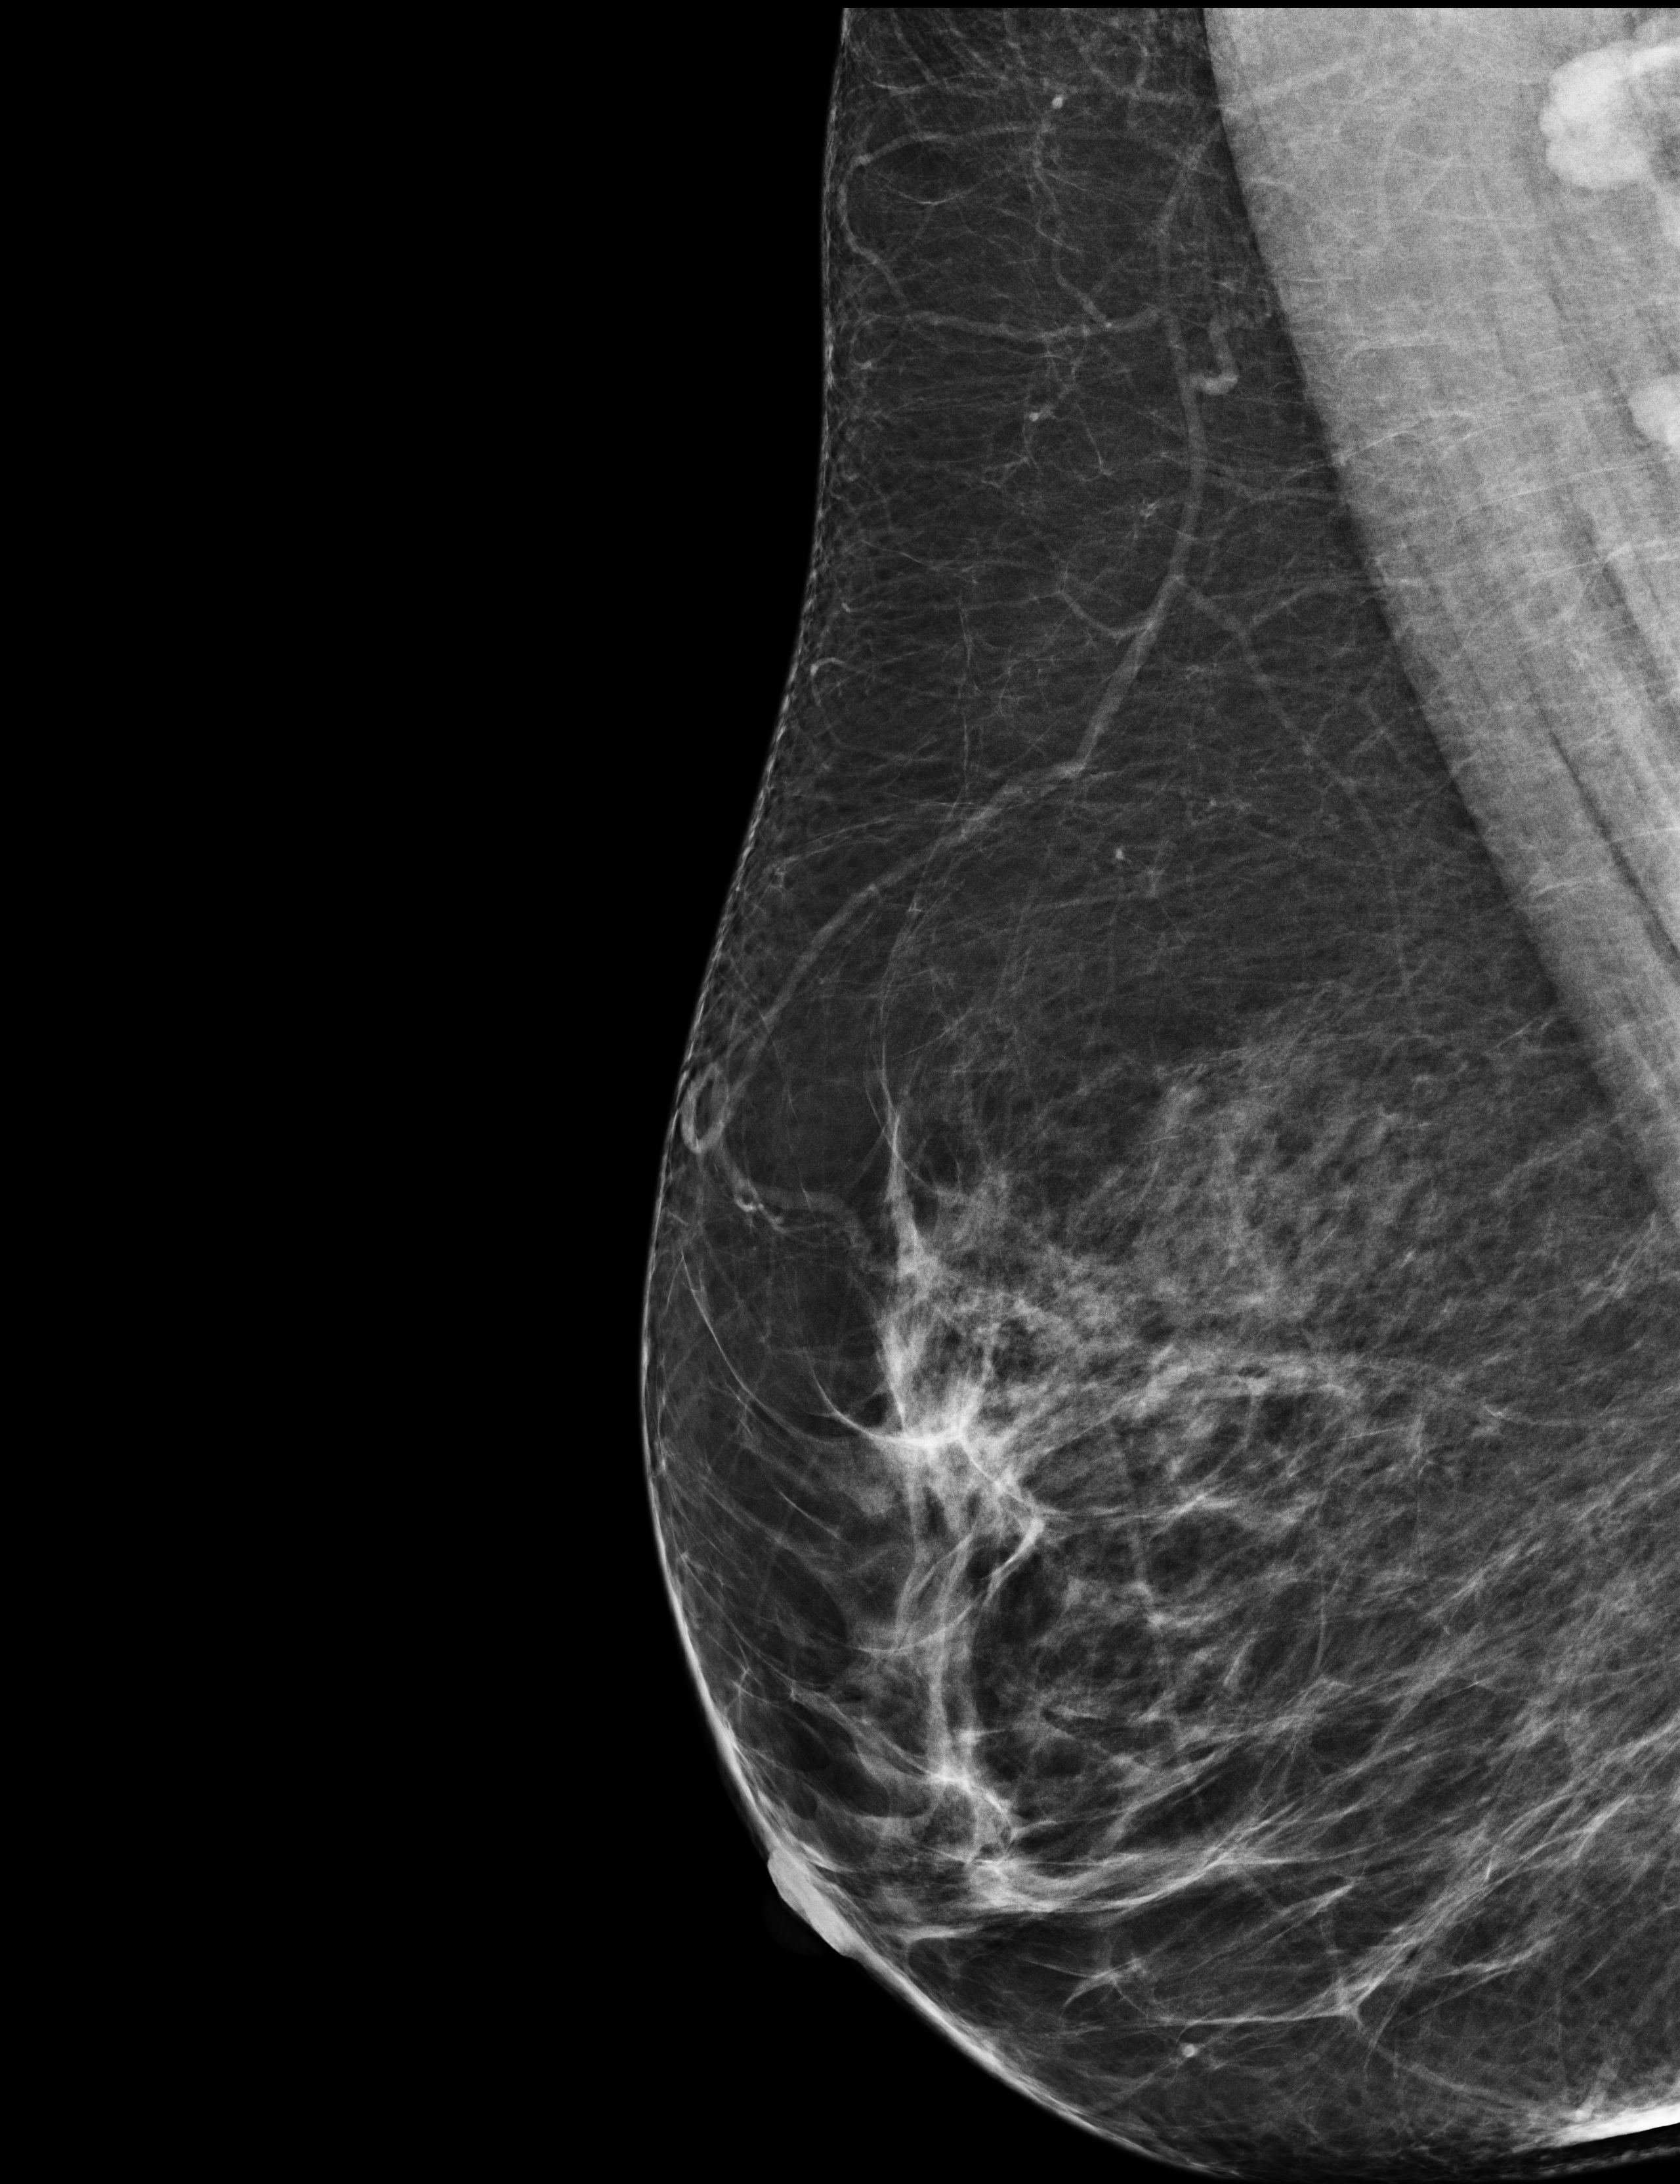
Annual screening mammography examination, system: Selenia Dimensions. Female patient, age 57 years.
Image type: full-field digital mammogram. Breast: right. Projection: medio-lateral oblique projection.